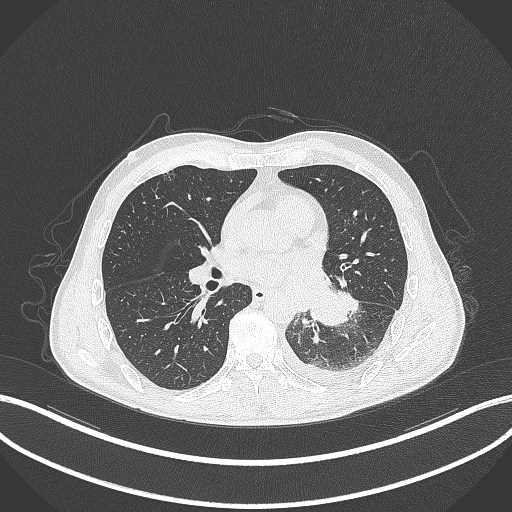
Chest CT, one axial slice; slice 153 of 295 in the series (ordered by position); reconstruction kernel B70f; 120 kVp; lung window (W 1500 / L -600 HU); 1 mm slice thickness; 512 × 512 image matrix, field of view 400 × 400 mm. Male patient, age 47 years. Case-level facts recorded for this patient, not image findings: clinical TNM (as recorded): T3 N1 M1c.
Outlined on this slice (rectangle marked by the reading radiologist):
- lung tumour (recorded histology: small cell carcinoma): bounding box <308,291,348,327> (left, top, right, bottom; pixels)